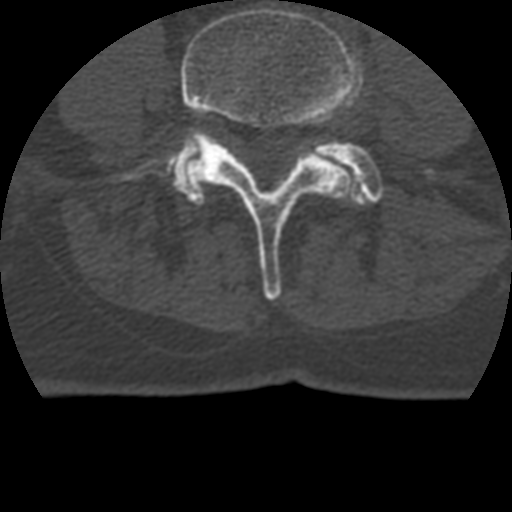
CT including the spine, one axial slice; position 61 of 399 along the scan axis; reconstruction kernel STANDARD; 120 kVp; bone window (W 1800 / L 400 HU); 512 × 512 image matrix, field of view 160 × 160 mm. Patient age 69 years. From the clinical record (not read from this slice): primary cancer: prostate.
Outlined on this slice (semi-automatically segmented with operator editing):
- L4 vertebra: bounding box <122,8,362,300> (left, top, right, bottom; pixels)
- L5 vertebra: <174,140,385,204>